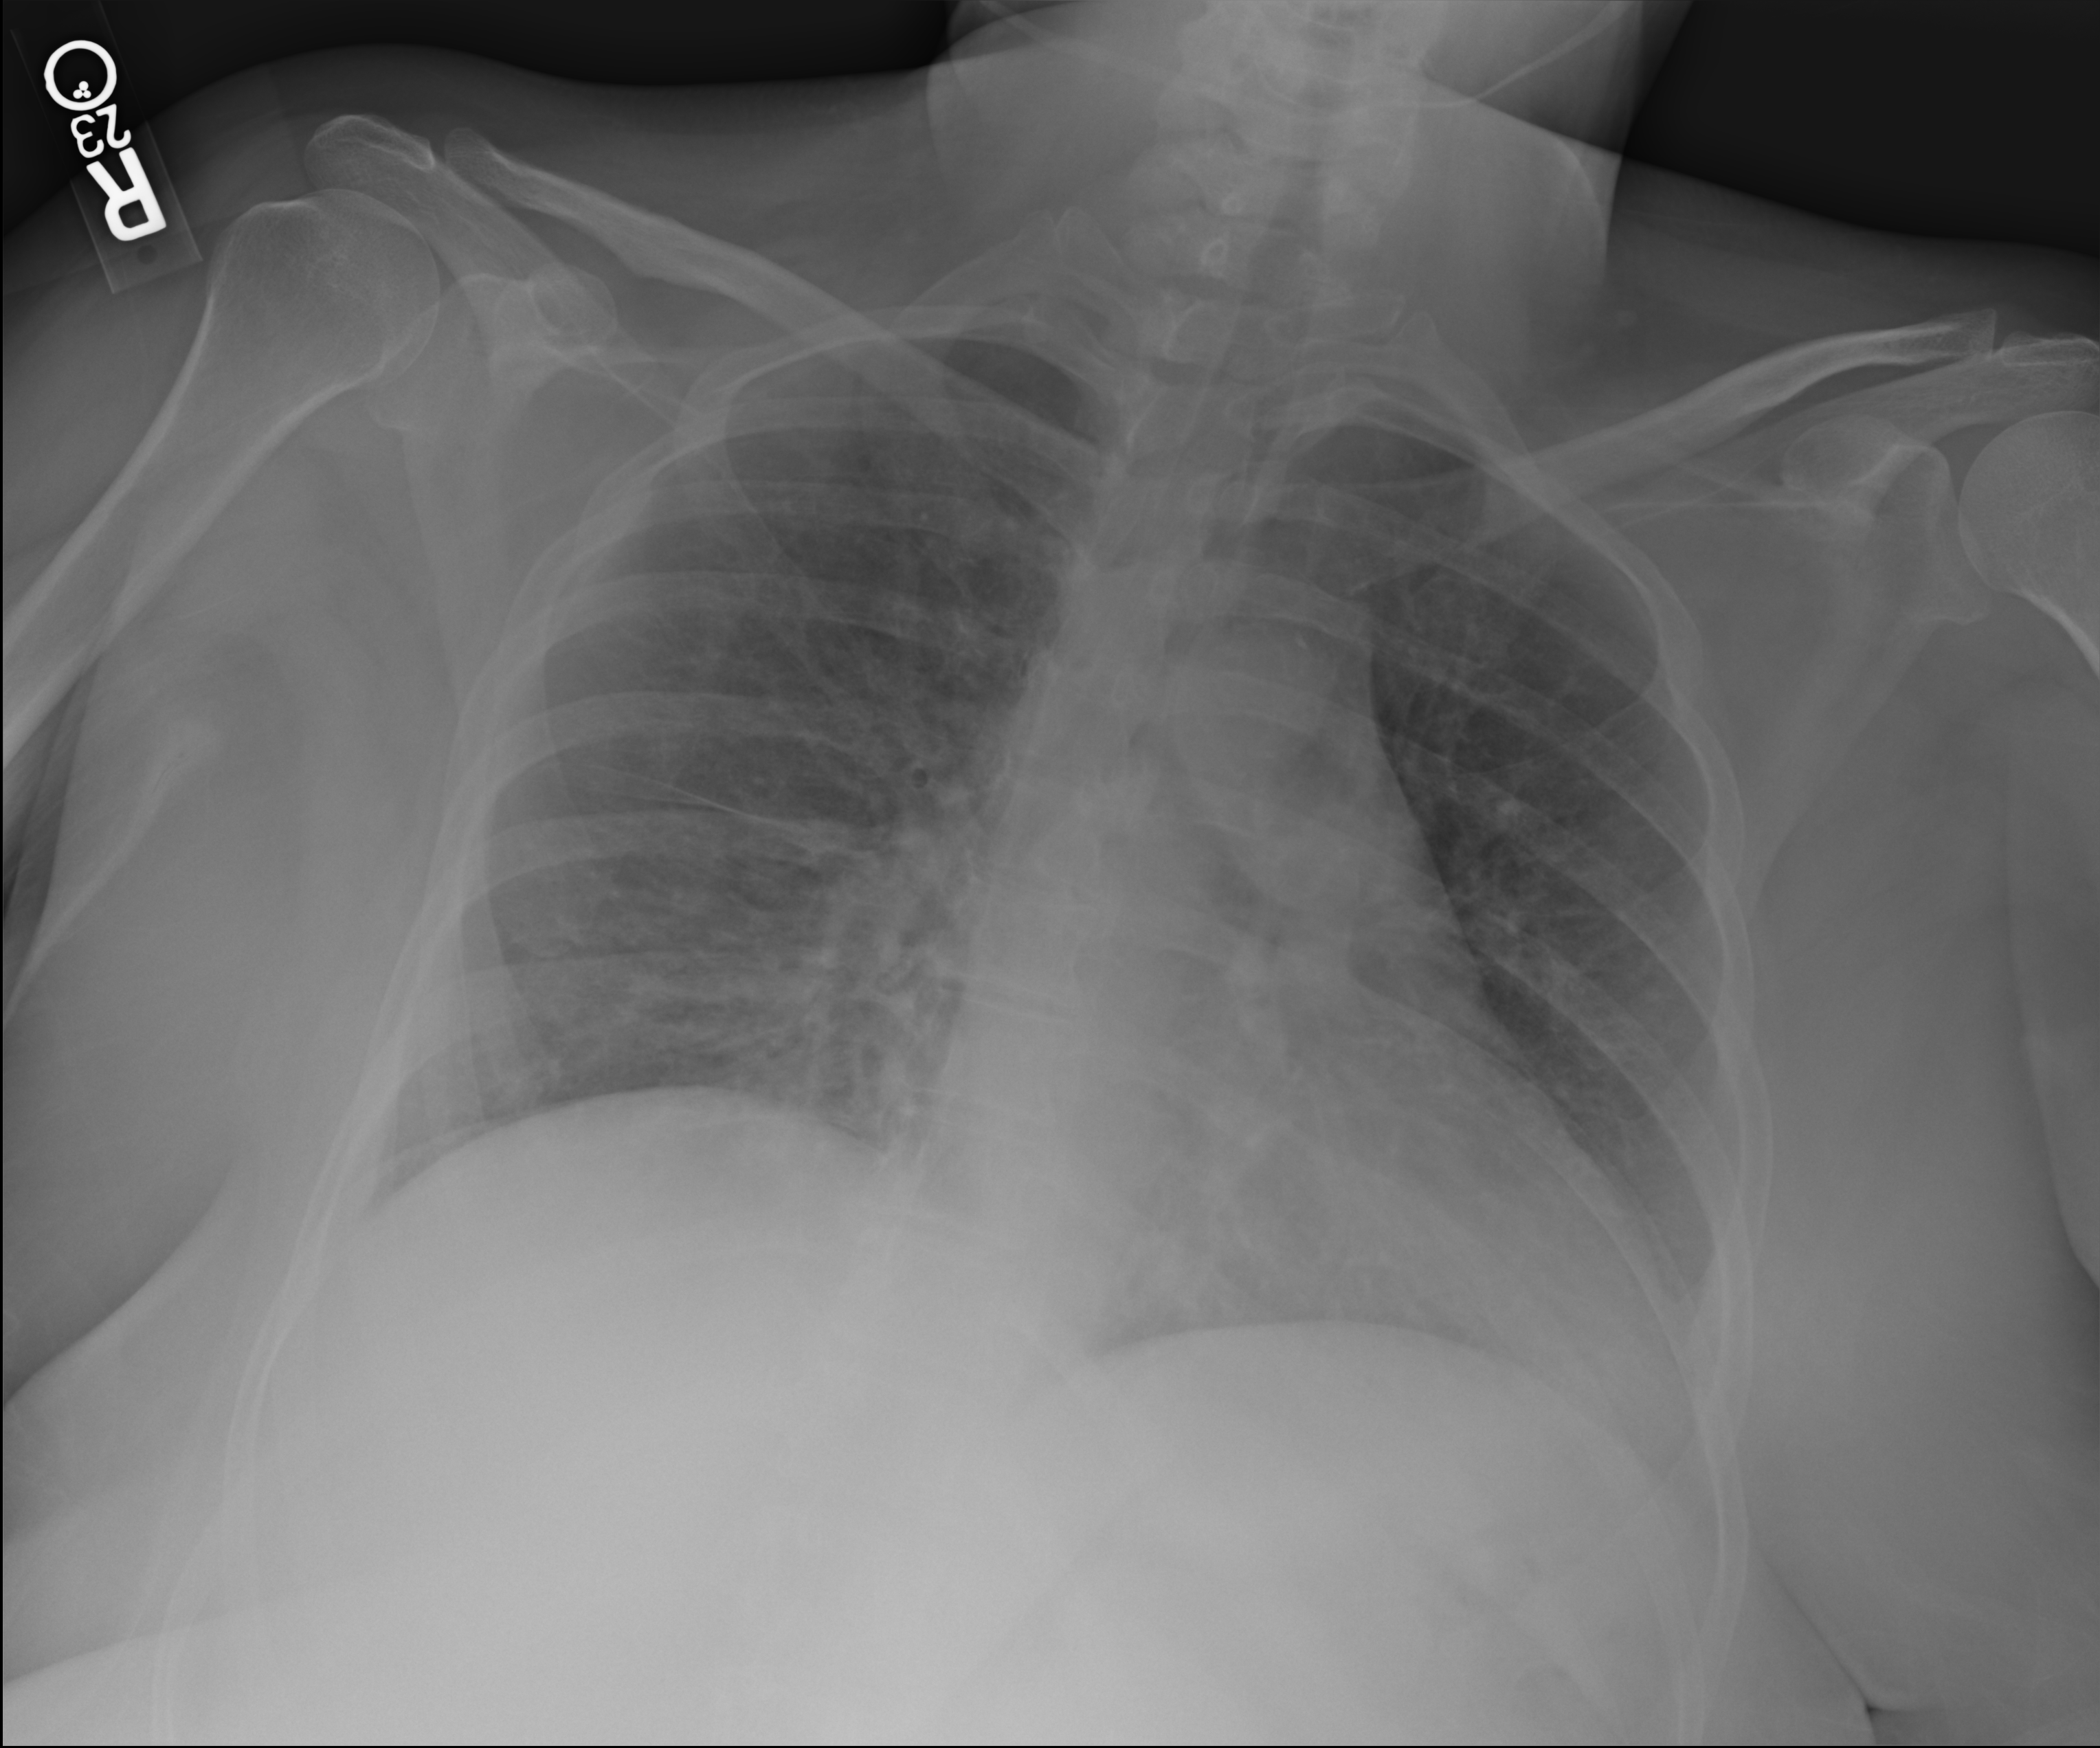
Chest X-ray (portable), anteroposterior (AP) projection. Patient hospitalised with COVID-19; female, aged 18–59 years.
Admission-level facts for this patient (not findings on this image; timing relative to this image not recorded): admitted to intensive care during this hospital stay: no; other chronic lung disease (admission record): yes; length of hospital stay: 8 days.